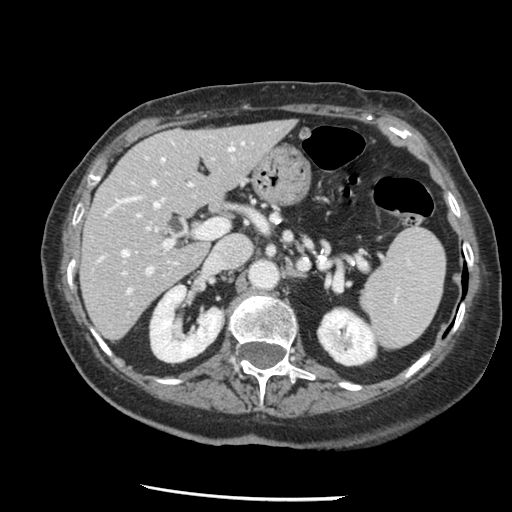
Contrast-enhanced abdominal CT, one axial slice. Position 79 of 148 along the scan axis. Reconstruction kernel STANDARD. 120 kVp. Intravenous contrast given. Soft-tissue window (W 400 / L 40 HU). 512 × 512 image matrix. Female patient, age 85 years. From the clinical record (not read from this slice): diagnosis: colorectal cancer liver metastases, imaged before liver resection; multiple liver metastases: no; largest metastasis: 0.9 cm; disease in both lobes: no.
Structures marked on this image (outlined manually by an expert reader):
- hepatic veins: bounding box <99,142,176,293> (left, top, right, bottom; pixels)
- liver: <82,121,294,339>
- planned liver remnant (the part of the liver to remain after resection): <82,121,294,339>
- portal vein (with intrahepatic branches): <122,145,230,276>